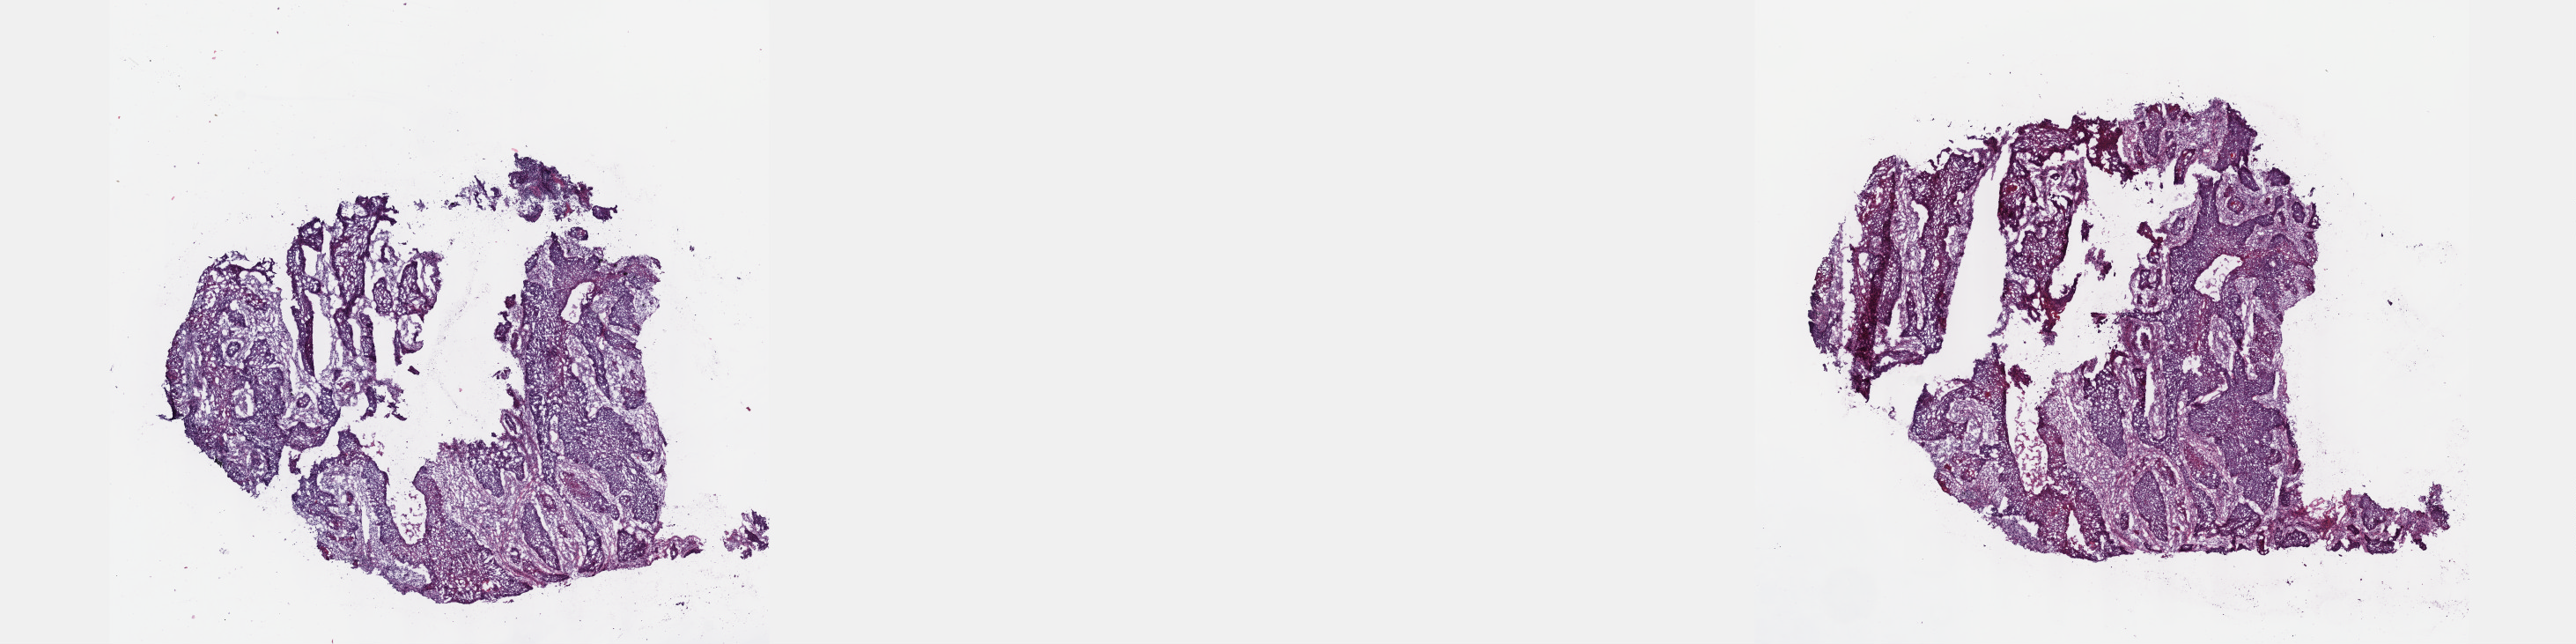
Hematoxylin and eosin (H&E) stained whole-slide image, whole scanned area (about 23.6 x 5.9 mm, acquisition: 40x scan) shown as a low-resolution overview. Frozen section from the top of the tissue portion. Sample: primary tumour, lung. Patient sex: male.
Pathologic diagnosis: Squamous cell carcinoma, NOS.